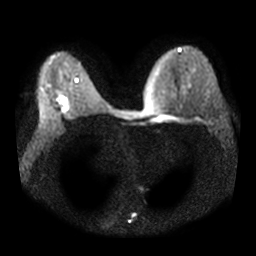
Breast MRI, one axial slice; position 19 of 31 along the scan axis; diffusion-weighted series; image 2 of 4 stored at this slice position (different b-values; order by instance number); 3 T; 256 × 256 image matrix, field of view 340 × 340 mm. Female patient.
Structures marked on this image (expert manual segmentation):
- tumour on diffusion-weighted imaging: bounding box <62,97,66,103> (left, top, right, bottom; pixels)